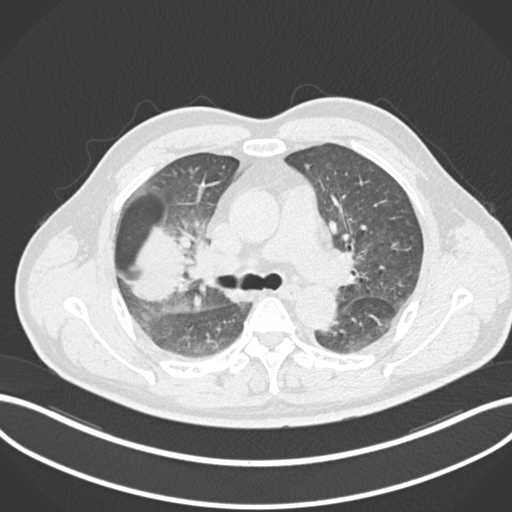
Chest CT, one axial slice. Slice 647 of 852 in the series (ordered by position). Reconstruction kernel B30f. 120 kVp. Lung window (W 1500 / L -600 HU). 1 mm slice thickness. 512 × 512 image matrix, field of view 400 × 400 mm. Patient: male, 55 years. Case-level facts recorded for this patient, not image findings: clinical TNM (as recorded): T3 N2 M1.
Structures marked on this image (bounding box drawn by a radiologist):
- lung tumour (recorded histology: adenocarcinoma): bounding box (x1, y1, x2, y2) in pixels: (118, 220, 188, 307)